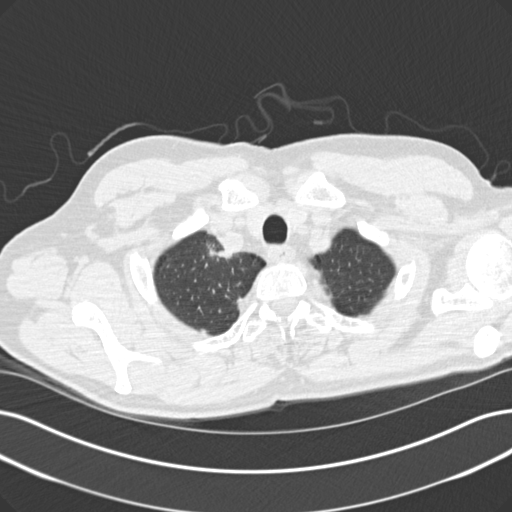
Low-dose screening chest CT, one axial slice; position 133 of 152 along the scan axis; lung window (W 1500 / L -600 HU); 2 mm slice thickness; 512 × 512 image matrix, field of view 365 × 365 mm.
Structures marked on this image (expert manual segmentation):
- lesion 1 (tumor, upper lobe of right lung): bounding box <208,245,228,260> (left, top, right, bottom; pixels)